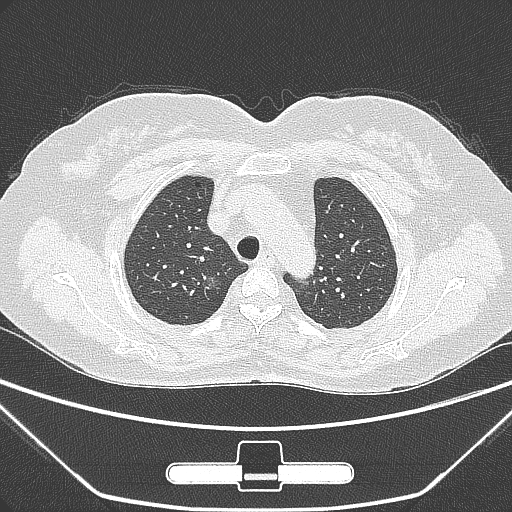
Chest CT, one axial slice; position 223 of 275 along the scan axis; lung window (W 1500 / L -600 HU); 512 × 512 image matrix, field of view 356 × 356 mm. Patient: female, 63 years. Case-level facts recorded for this patient, not image findings: clinical TNM (as recorded): T1a N0 M0.
Annotated regions visible in this slice (rectangle marked by the reading radiologist):
- lung tumour (recorded histology: adenocarcinoma): box from (x=195, y=271) to (x=221, y=293) px